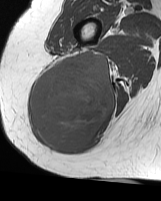
MRI of an extremity soft-tissue mass, one axial slice. Position 30 of 70 along the scan axis. MR volume resampled by the dataset authors to the PET/CT grid (not the native acquisition matrix). 161 × 201 image matrix. Female patient. Case-level facts recorded for this patient, not image findings: histological type: synovial sarcoma; grade: intermediate; site of the primary tumour: right buttock.
Outlined on this slice (expert contour drawn on MRI and transferred to this co-registered scan by the dataset authors):
- gross tumour volume including surrounding oedema: bounding box [x1, y1, x2, y2] px = [31, 52, 116, 153]
- gross tumour volume (mass): [31, 52, 116, 153]